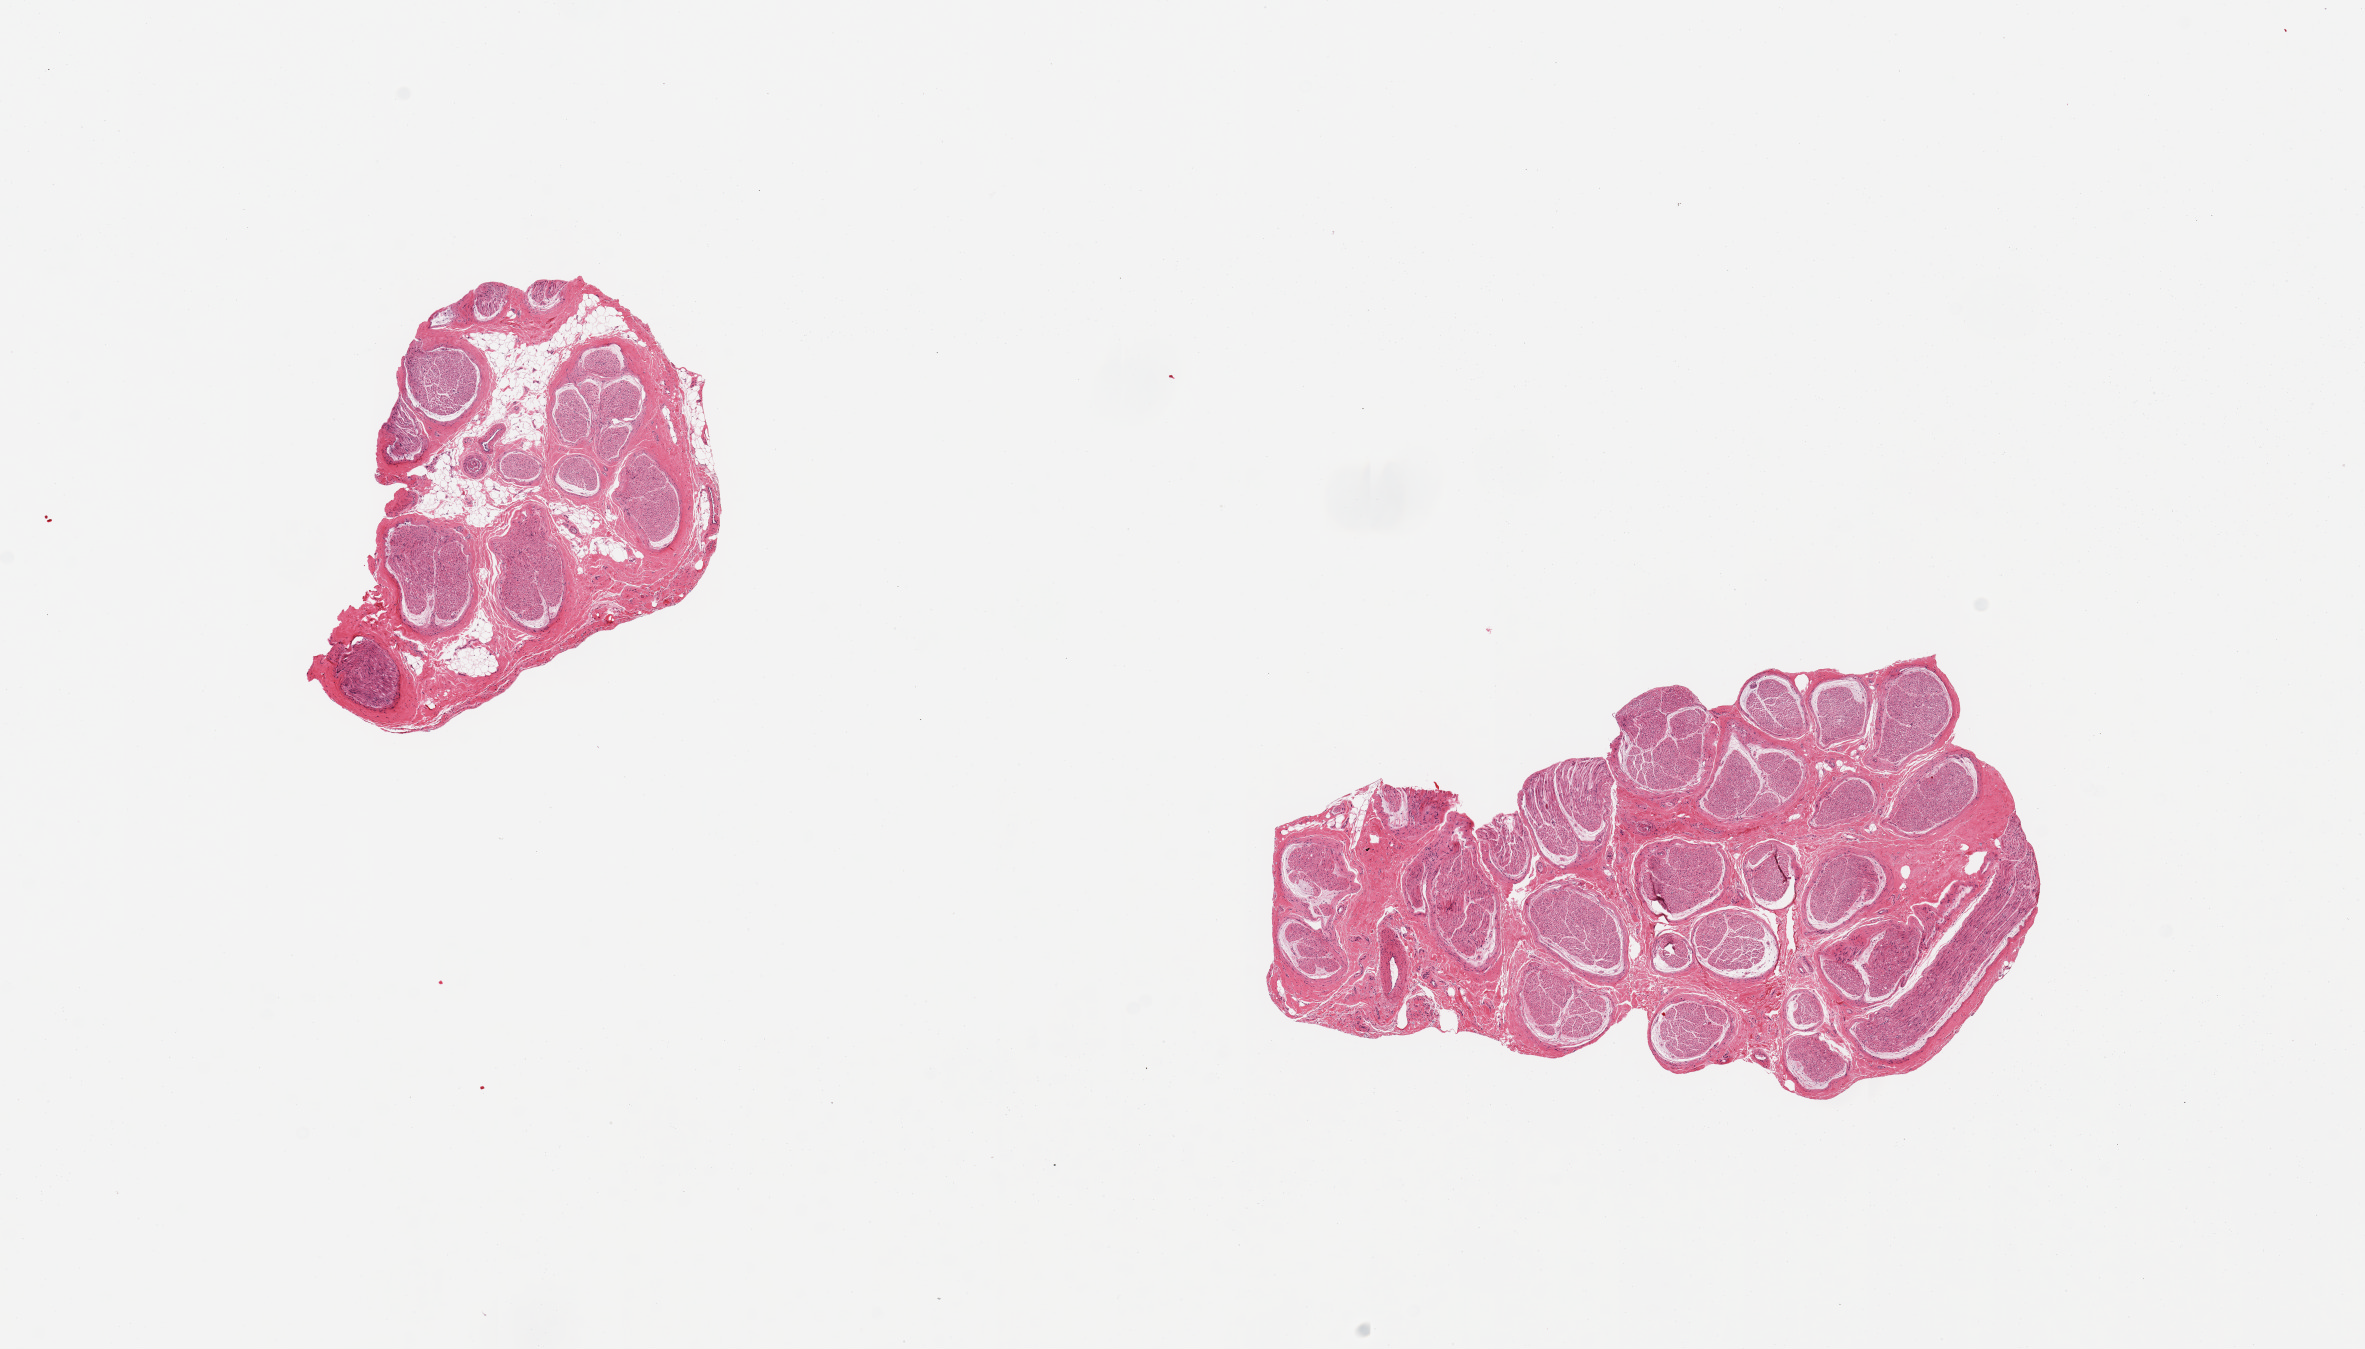
Digitized haematoxylin and eosin-stained section, shown as a low-resolution overview of the whole scanned area (about 18.7 x 10.7 mm); PAXgene-fixed, paraffin-embedded tissue; target tissue: tibial nerve; tissue donor sample.
• reviewer comment on this tissue sample: 2 pieces, excellent clean specimens